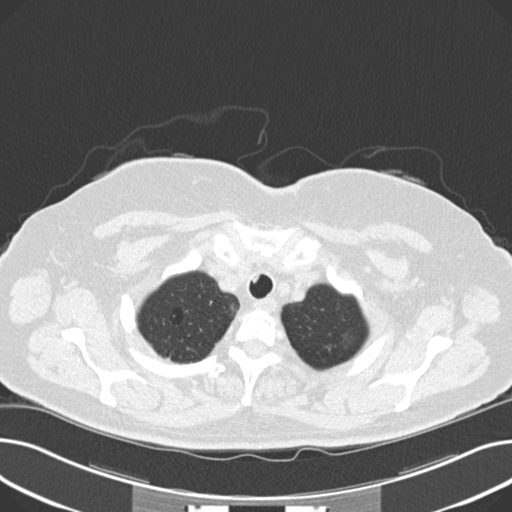
Low-dose screening chest CT, axial slice; third annual screen; lung window (W 1500 / L -600 HU); 2 mm slice thickness; standard (soft-tissue) reconstruction kernel (B30f); slice 29 of 203 in the series. Female, age 60 years at enrolment. Current smoker at enrolment.
Expert reader's lesion annotation, bounding box [x1, y1, x2, y2] px = [323, 327, 371, 359]. The screening reader recorded 8 non-calcified nodules or masses ≥4 mm on this exam (right upper lobe, lingula, lingula, right middle lobe, right lower lobe, left lower lobe, left lower lobe, left lower lobe); which of them this box marks is not recorded. Lung cancer was diagnosed 176 days after this screen: non-small cell carcinoma, left upper lobe, poorly differentiated (G3), stage IB (AJCC 6th edition), 7 mm at pathology.